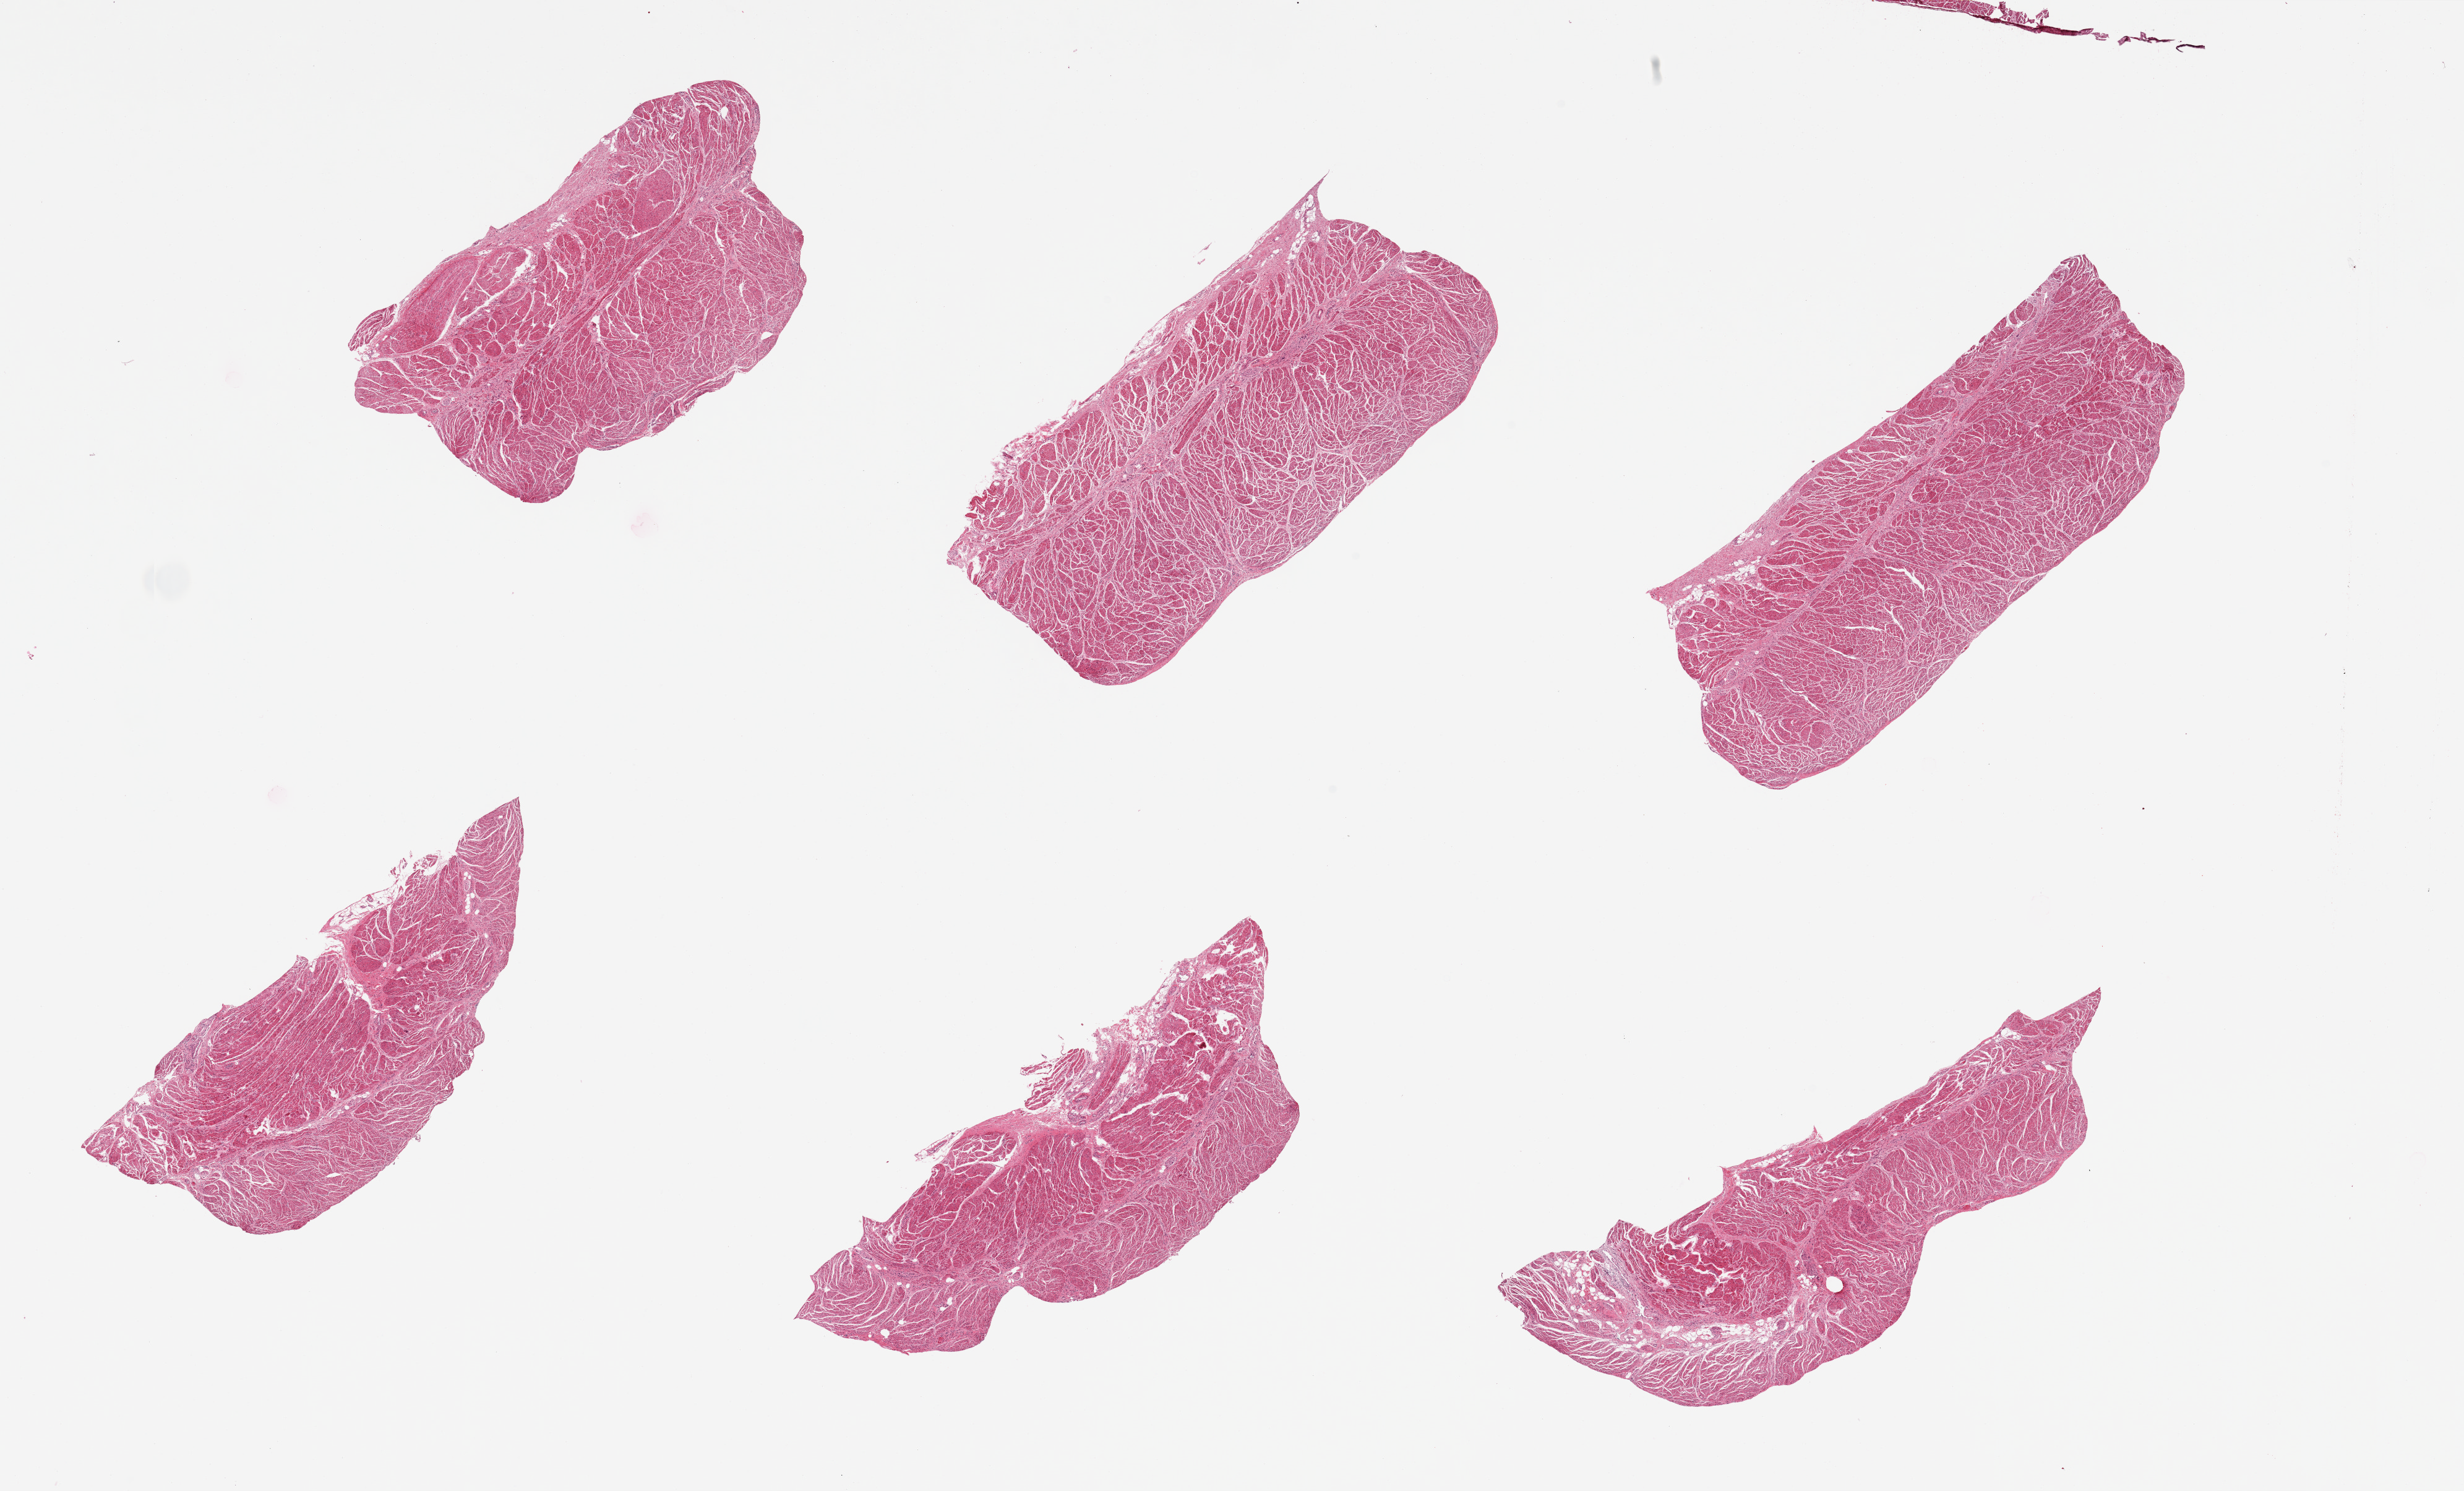
Haematoxylin and eosin whole-slide image, a low-resolution overview of the entire scanned area, about 31.5 x 19.1 mm, PAXgene-fixed paraffin-embedded (PFPE) section, section of gastroesophageal junction (target tissue), donor tissue sample. Donor: female.
- pathologist's review note for this sample: 6 pieces, well trimmed